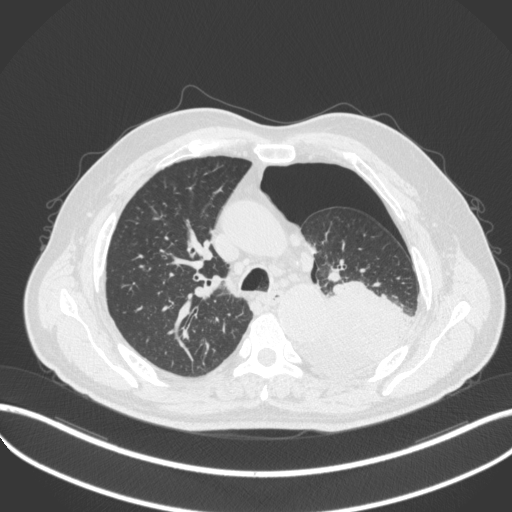
Chest CT, one axial slice; slice 354 of 466 in the series (ordered by position); reconstruction kernel B31f; 120 kVp; lung window (W 1500 / L -600 HU); 1 mm slice thickness; 512 × 512 image matrix. Patient: male, 76 years. From the clinical record (not read from this slice): clinical TNM (as recorded): T3 N0 M1b.
Annotated regions visible in this slice (bounding box drawn by a radiologist):
- lung tumour (recorded histology: adenocarcinoma): bounding box <295,278,422,378> (left, top, right, bottom; pixels)